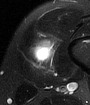
MRI of an extremity soft-tissue mass, one axial slice; position 14 of 65 along the scan axis; T2-weighted fat-saturated; MR volume resampled by the dataset authors to the PET/CT grid (not the native acquisition matrix); 3.27 mm slice thickness; 90 × 105 image matrix, field of view 88 × 103 mm. Male patient. From the clinical record (not read from this slice): histological type: mixoid liposarcoma; grade: low; site of the primary tumour: left thigh.
Structures marked on this image (expert contour drawn on MRI and transferred to this co-registered scan by the dataset authors):
- gross tumour volume (mass): bounding box [x1, y1, x2, y2] px = [34, 44, 53, 63]